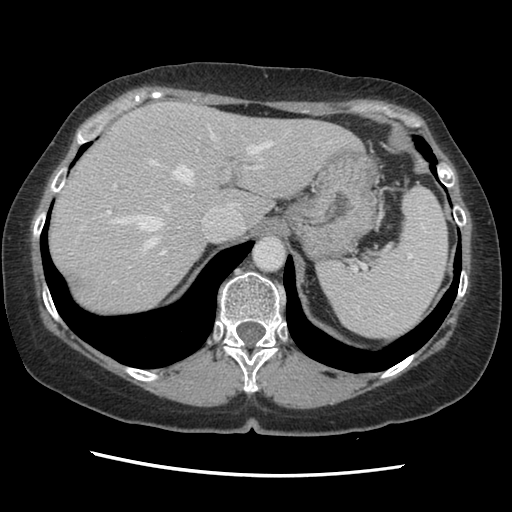
Contrast-enhanced abdominal CT, one axial slice; position 104 of 141 along the scan axis; 120 kVp; soft-tissue window (W 400 / L 40 HU); 512 × 512 image matrix. Female patient, age 61 years. From the clinical record (not read from this slice): diagnosis: colorectal cancer liver metastases, imaged before liver resection; multiple liver metastases: no; largest metastasis: 2.4 cm; disease in both lobes: no.
Structures marked on this image (outlined manually by an expert reader):
- hepatic veins: box from (x=81, y=127) to (x=316, y=289) px
- liver: (x=50, y=102)–(x=359, y=317)
- planned liver remnant (the part of the liver to remain after resection): (x=49, y=102)–(x=359, y=317)
- portal vein (with intrahepatic branches): (x=101, y=149)–(x=263, y=254)